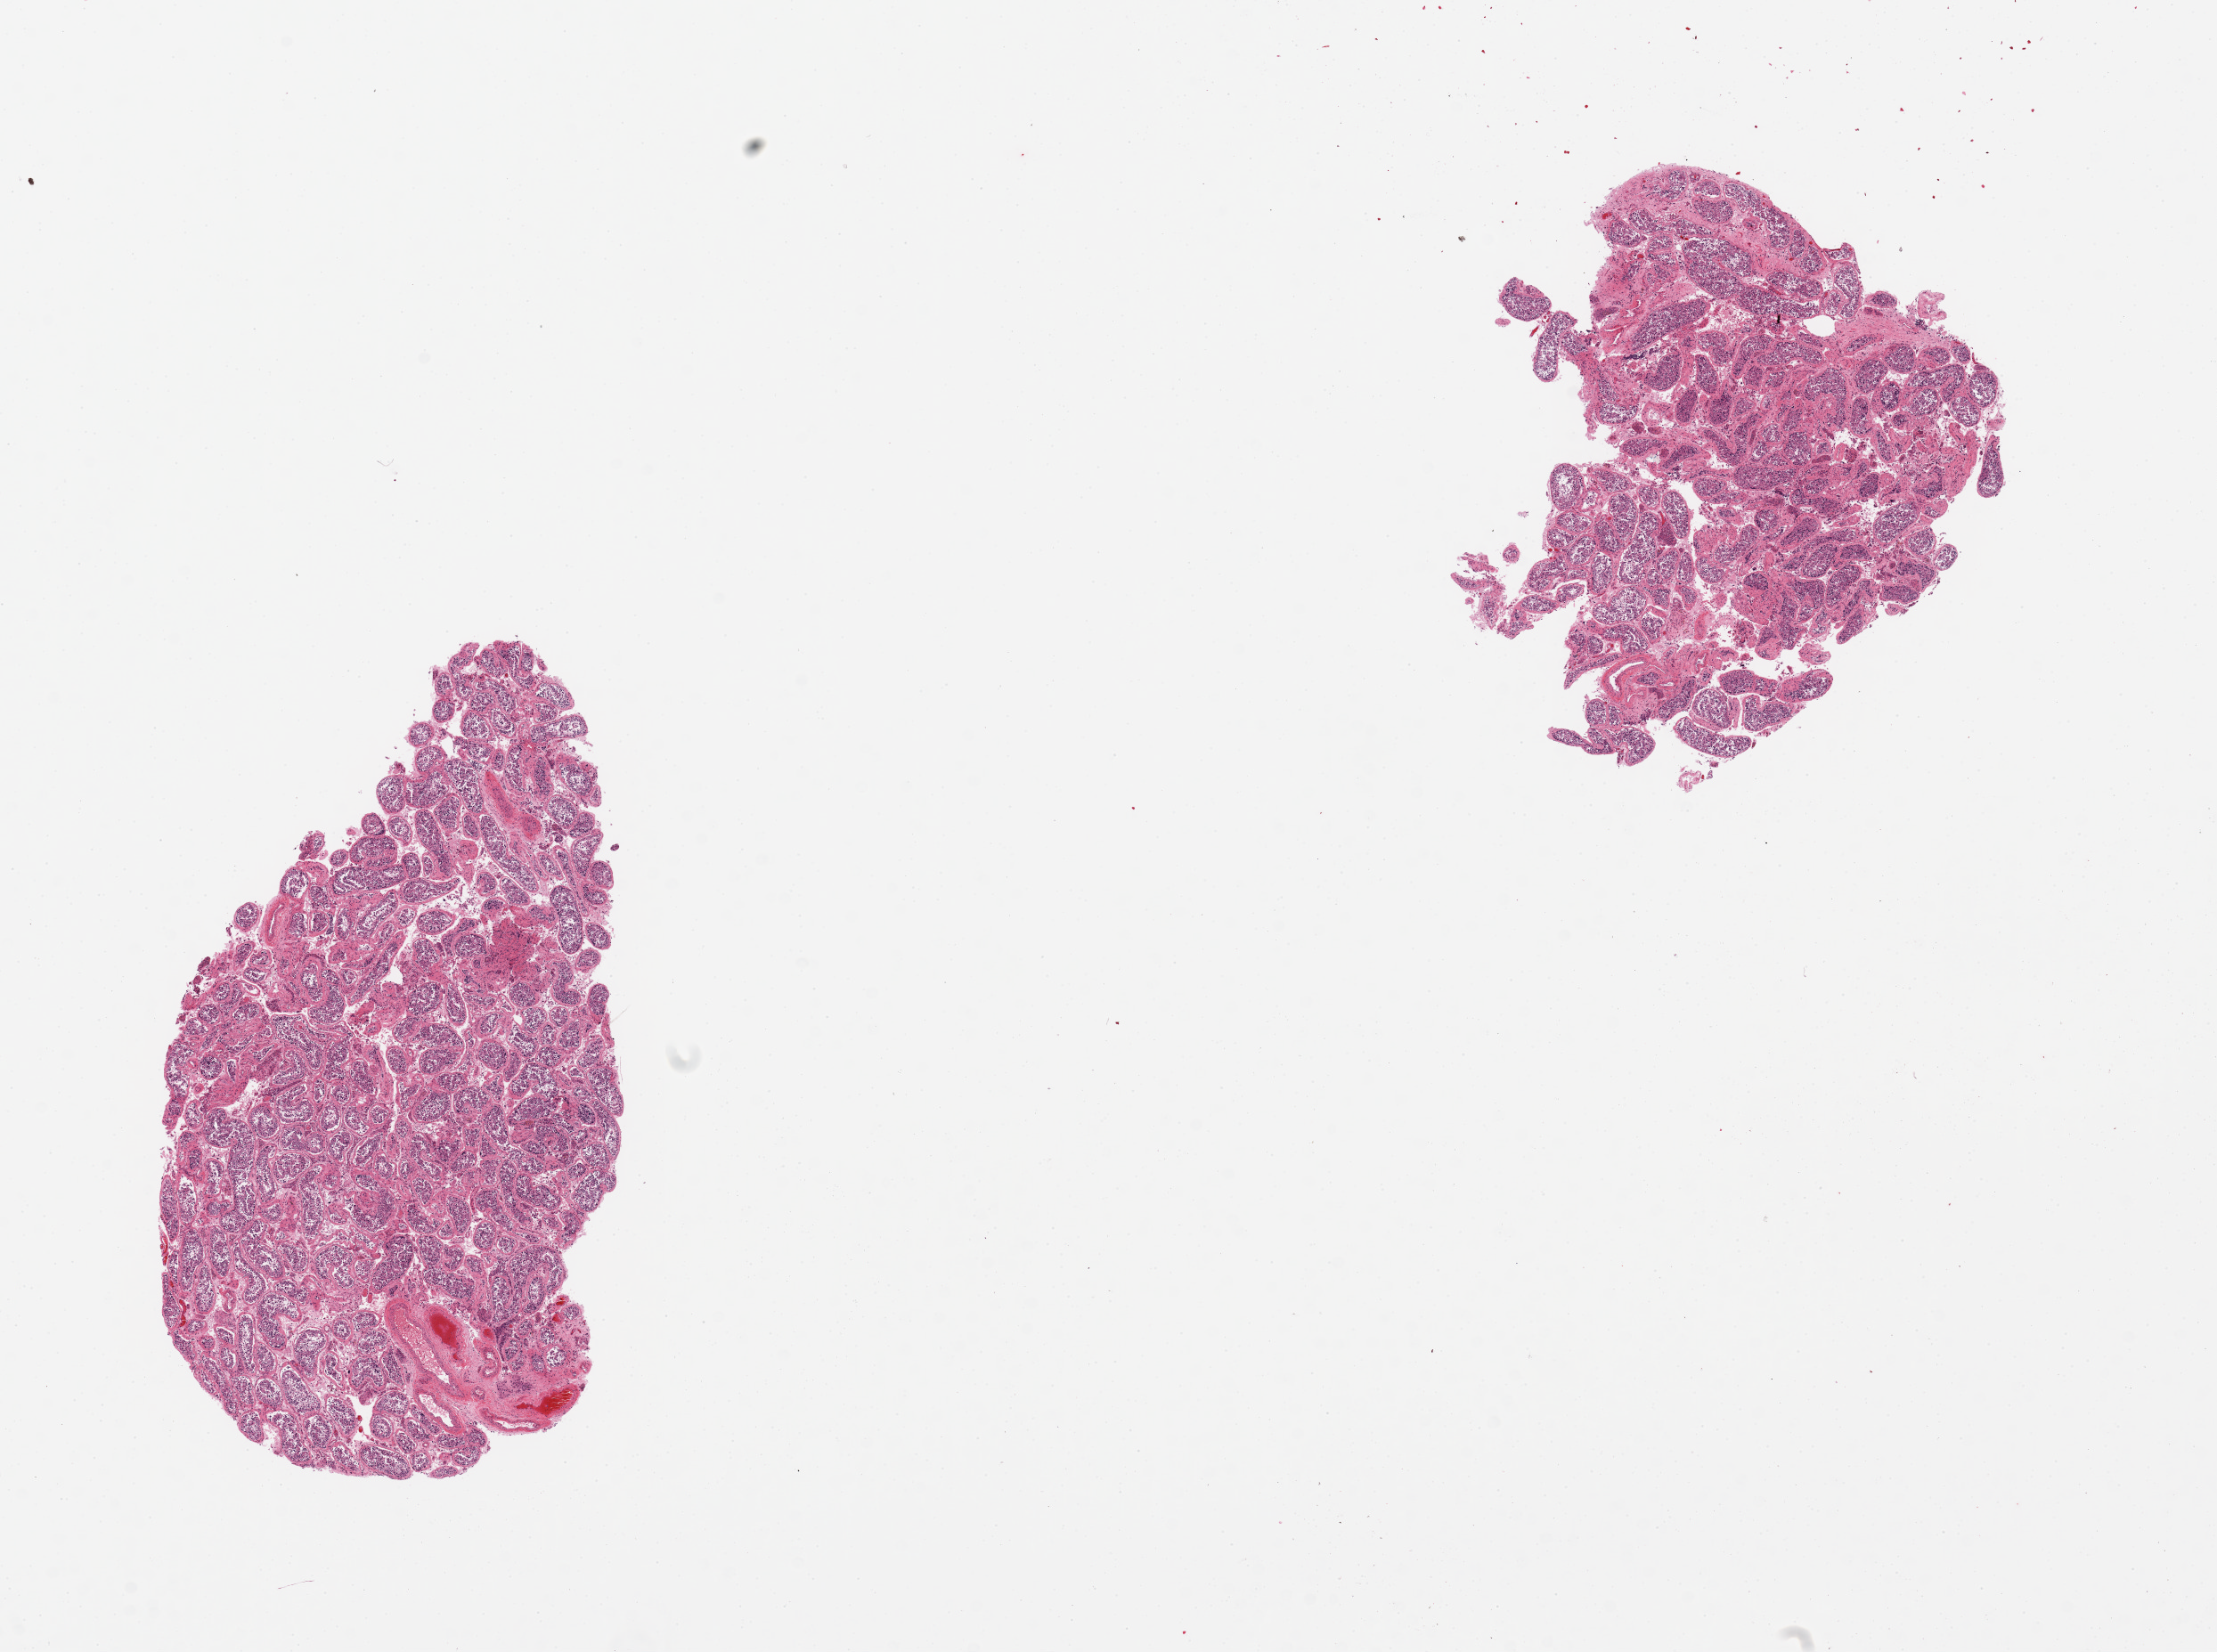
Digitized haematoxylin and eosin-stained section, brightfield — whole scanned area (about 19.7 x 14.7 mm, from a 20x scan) shown as a low-resolution overview, PAXgene-fixed paraffin-embedded (PFPE) section, section of testis (target tissue), tissue donor sample. Donor sex: male.
Pathologist's review note for this sample: 2 pieces, active spermatogenesis.